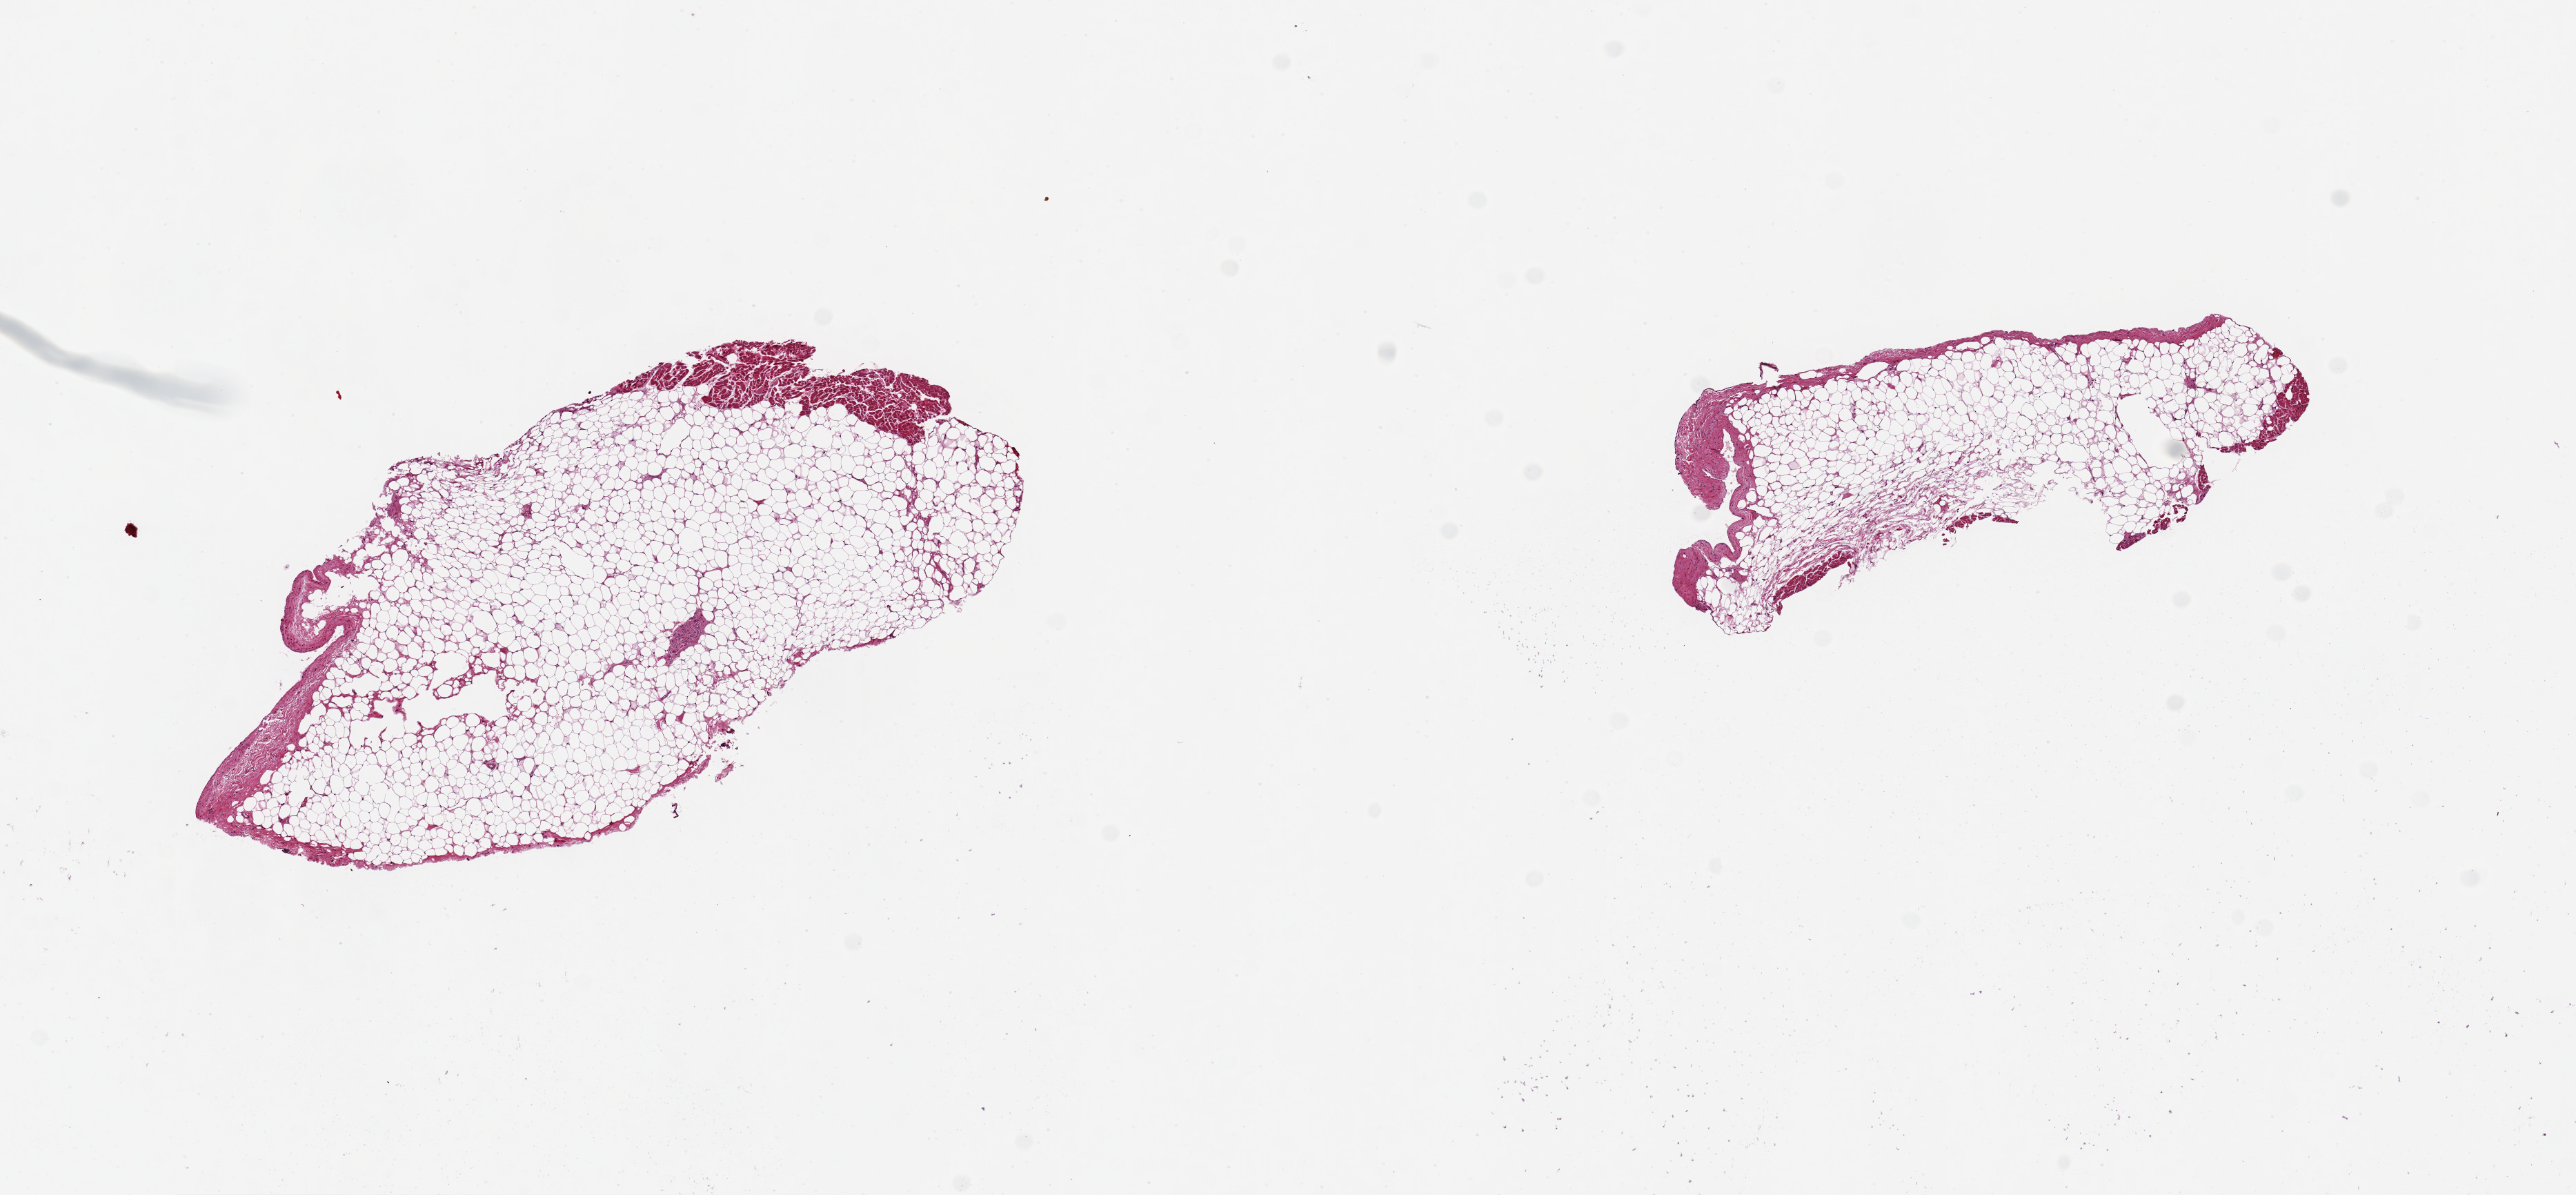
Whole-slide image, hematoxylin and eosin (H&E) stain — a low-resolution overview of the entire scanned area, about 14.8 x 6.8 mm (slide scanned at 20x); PAXgene-fixed paraffin-embedded (PFPE) section; target tissue: coronary artery; donor tissue sample. Male donor.
* reviewer comment on this tissue sample: 2 pieces 5x2 & 4x1 mm; NO ARTERY; all adipose and focal myocardium